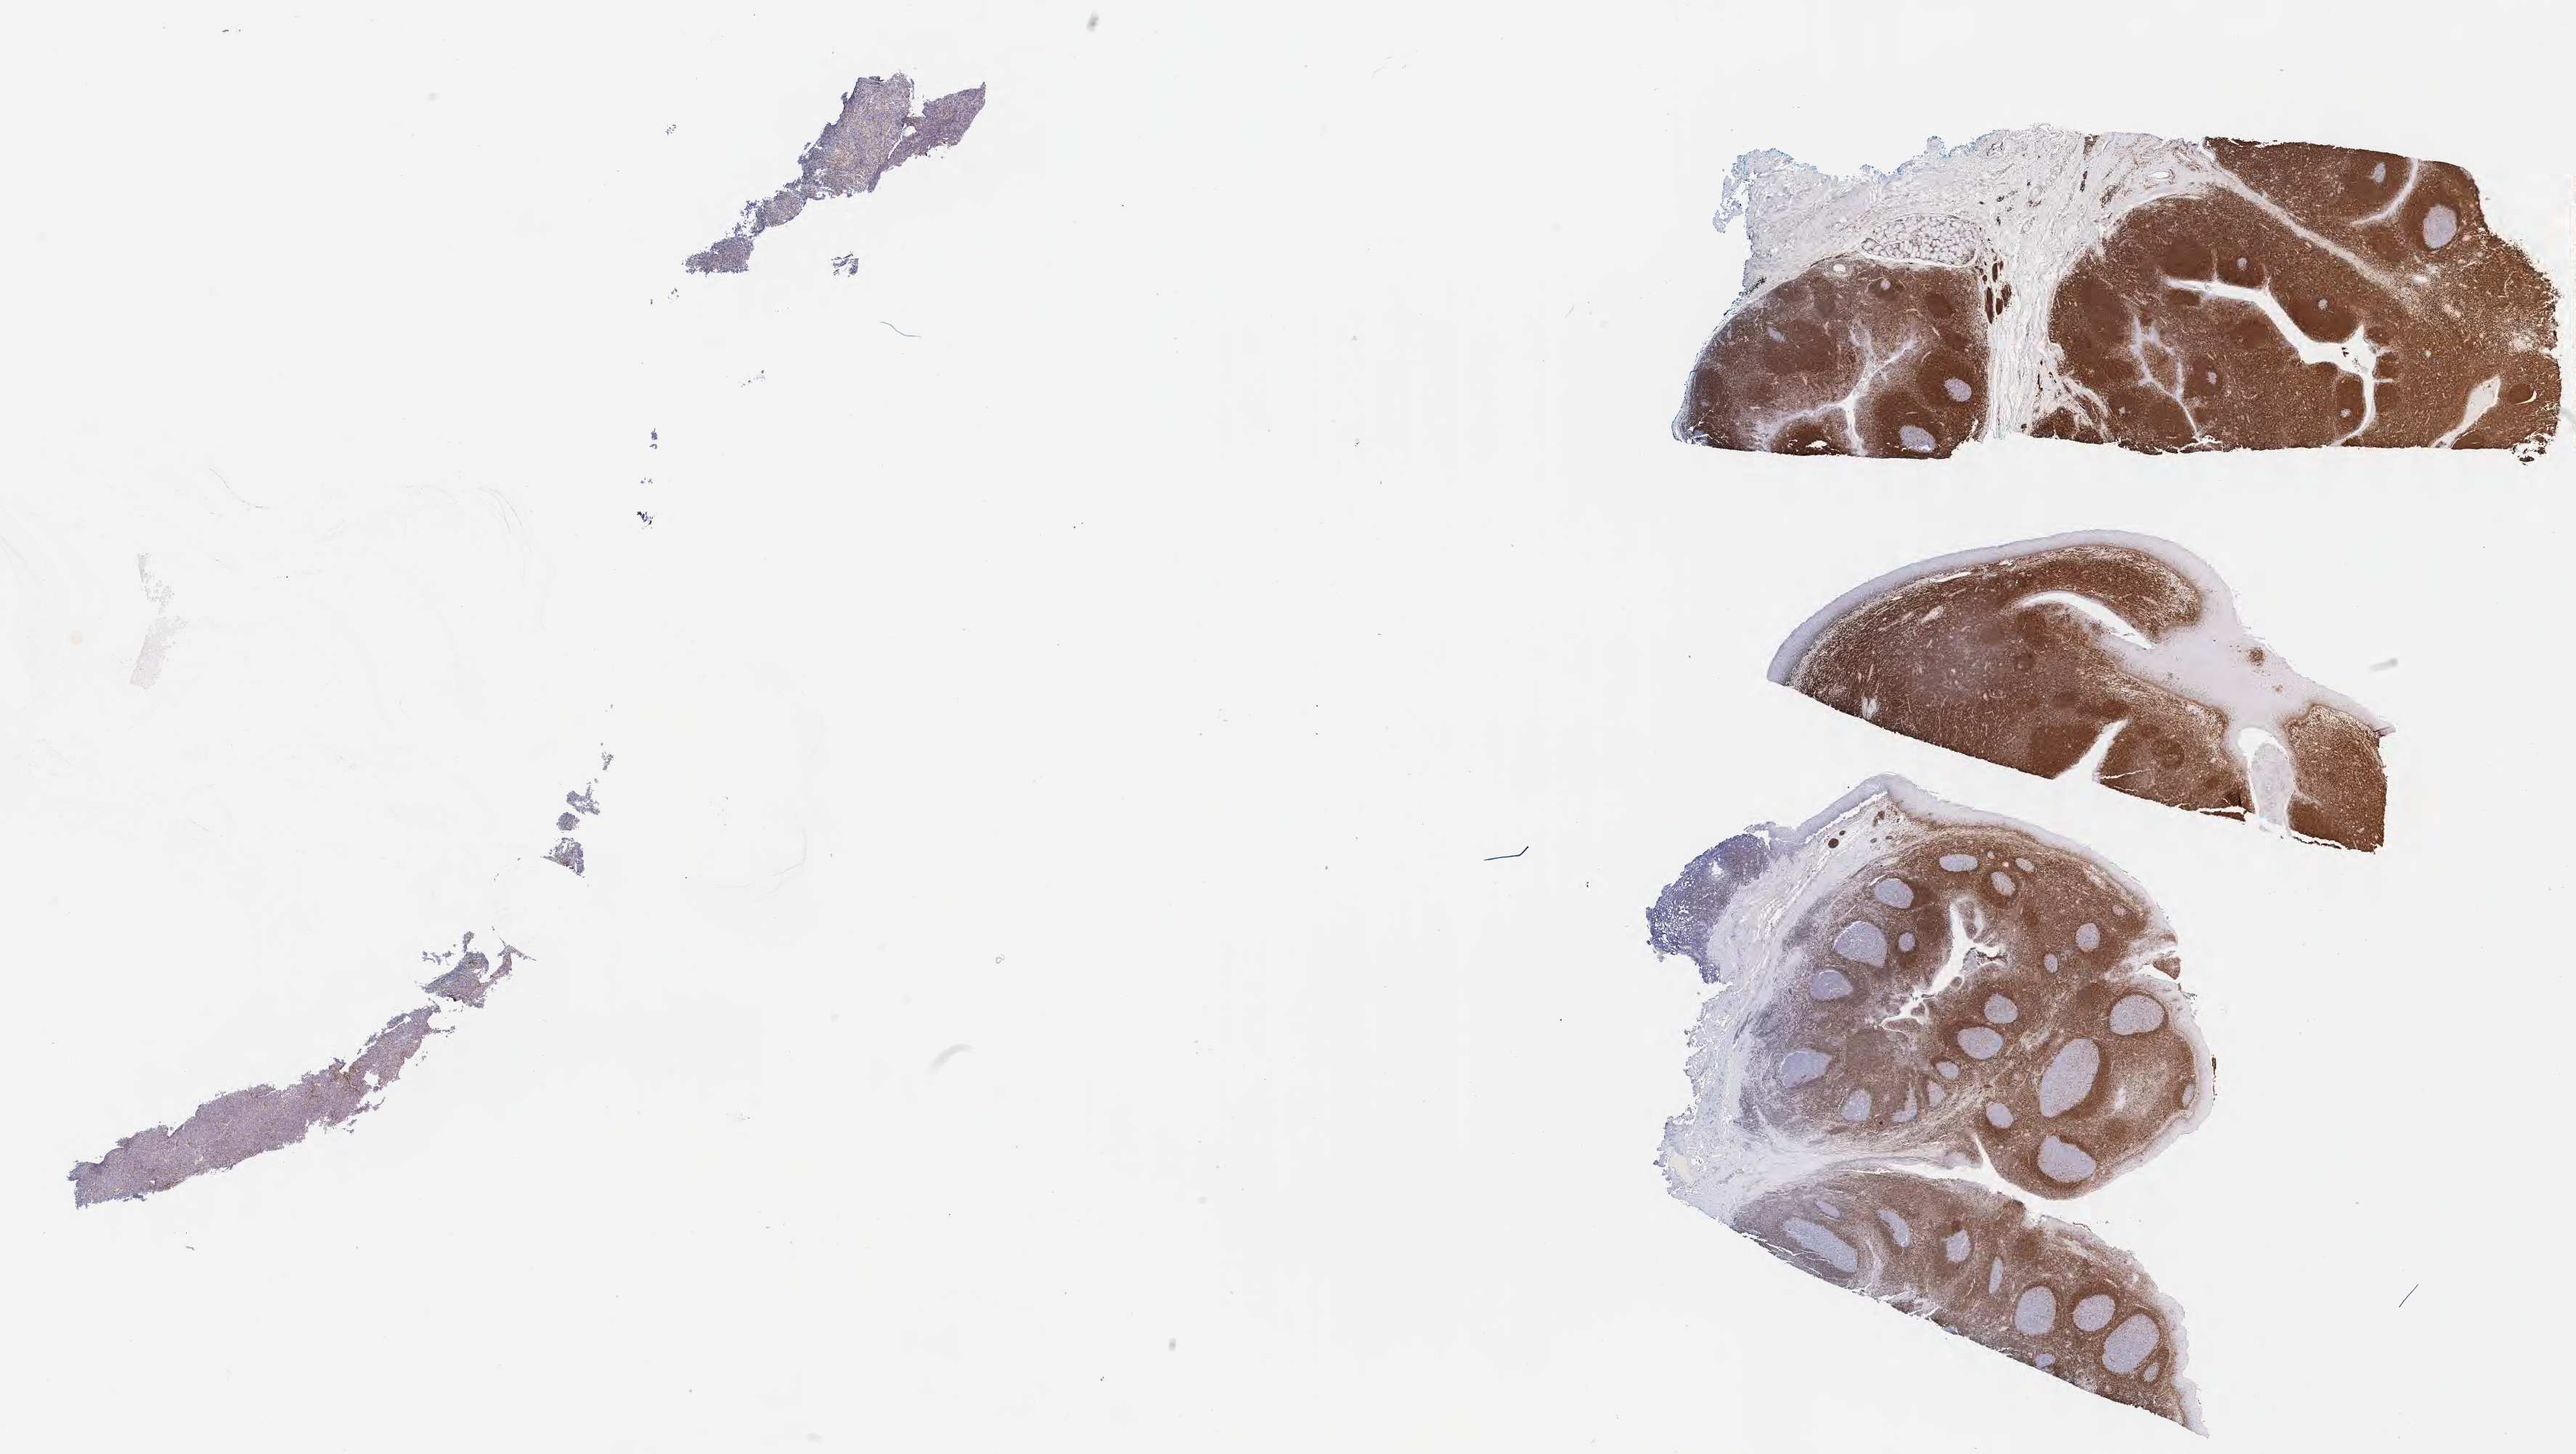
IHC for BCL2, whole-slide image, shown as a low-resolution overview of the whole scanned area (about 28.7 x 16.2 mm), specimen: tumor tissue, site: cranium. Patient: female, age at initial diagnosis 7 years.
Diagnosis: Burkitt lymphoma, NOS.